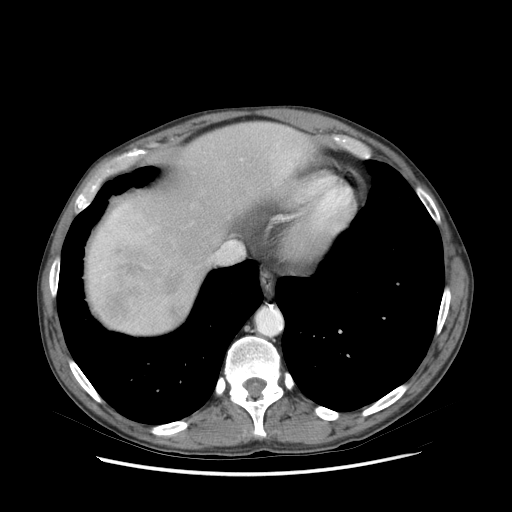
Contrast-enhanced abdominal CT (liver protocol), one axial slice; slice 70 of 89 in the series (ordered by position); reconstruction kernel STANDARD; soft-tissue window (W 400 / L 40 HU); 2.5 mm slice thickness; 512 × 512 image matrix. From the clinical record (not read from this slice): diagnosis: hepatocellular carcinoma (patient treated with transarterial chemoembolisation; whether this scan precedes or follows treatment is not stated here); TNM stage (as recorded): Stage-IIIB; Child-Pugh class: A.
Structures marked on this image (semi-automatic segmentation, software-assisted and operator-edited):
- abdominal aorta: bounding box (x1, y1, x2, y2) in pixels: (258, 308, 281, 335)
- liver parenchyma outside the tumour (the mass and vessels are separate outlines, so this box may not span the whole liver): (86, 122, 312, 334)
- mass: (92, 243, 186, 321)
- liver vessels: (92, 155, 292, 282)